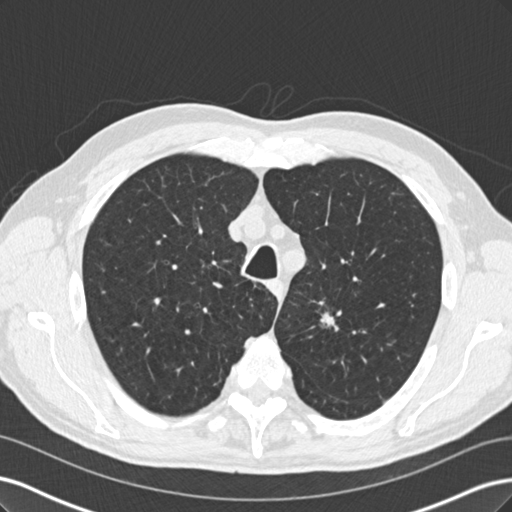
Low-dose screening chest CT, one axial slice. Position 175 of 219 along the scan axis. Reconstruction kernel B30f. 120 kVp. Lung window (W 1500 / L -600 HU). 2 mm slice thickness. 512 × 512 image matrix, field of view 360 × 360 mm.
Structures marked on this image (outlined manually by an expert reader):
- lesion 1 (tumor, upper lobe of left lung): bounding box (x1, y1, x2, y2) in pixels: (320, 310, 342, 332)